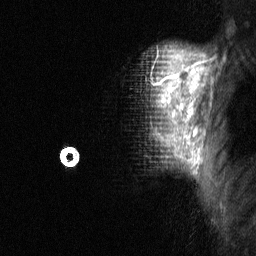
Breast MRI (dynamic contrast-enhanced), one sagittal slice; position 51 of 64 along the scan axis; dynamic contrast-enhanced study with each time point stored as its own series, time point 2 of 3 at this slice position (early post-contrast, ordered by acquisition time); 1.5 T; TE 4.8 ms, TR 27 ms; 2 mm slice thickness; 256 × 256 image matrix, field of view 180 × 180 mm. Patient: female, 36 years. From the clinical record (not read from this slice): setting: breast cancer imaged before/during neoadjuvant chemotherapy; receptor status: HR-positive, HER2-negative.
Annotated regions visible in this slice (semi-automatically segmented with operator editing):
- analysis volume of interest (the breast-tissue region the enhancement analysis was run in; not a lesion): bounding box <67,44,211,177> (left, top, right, bottom; pixels)
- tumour enhancement mask (voxels above the 90 % enhancement threshold inside the analysis volume of interest): <162,63,202,163>